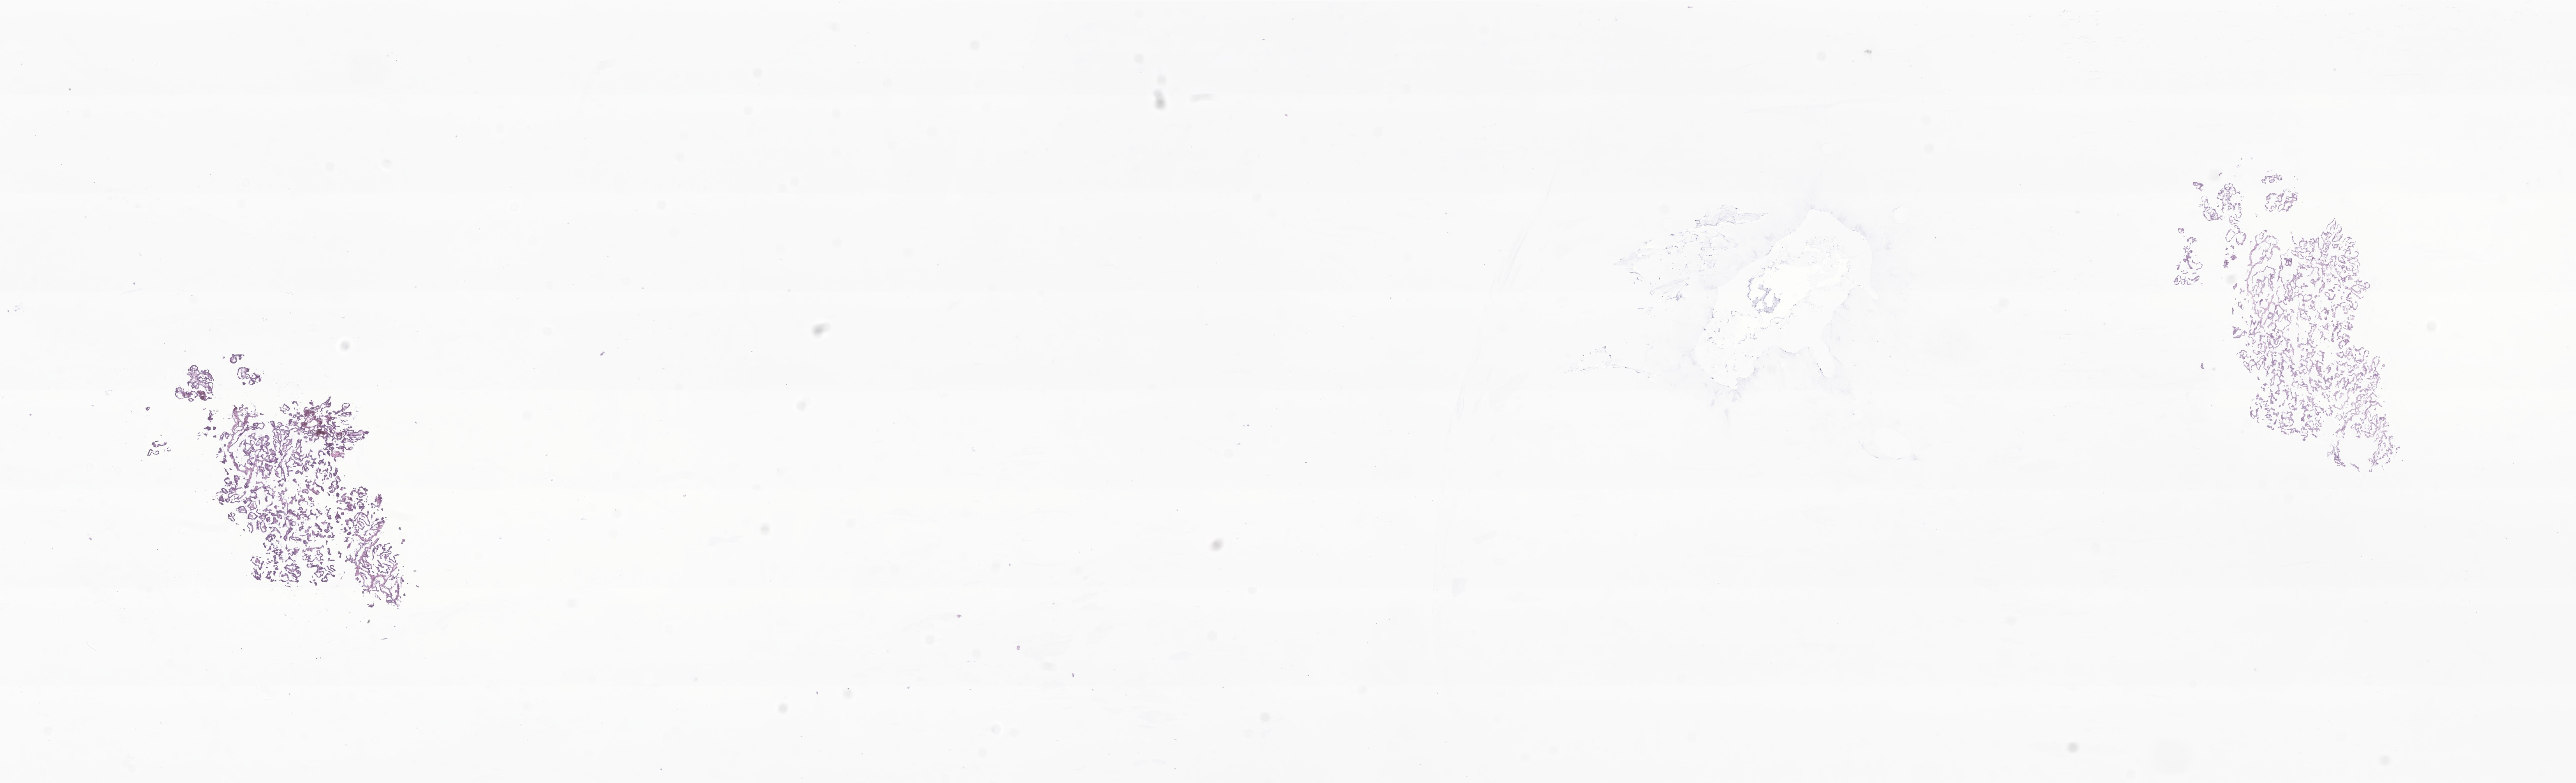
Haematoxylin and eosin whole-slide image of tumor tissue from the thyroid, low-resolution overview of the scanned area, about 27.9 x 8.5 mm. Frozen section (OCT-embedded). Female patient, age 131 months (10 years 11 months).
Recorded diagnosis: Papillary carcinoma, NOS.